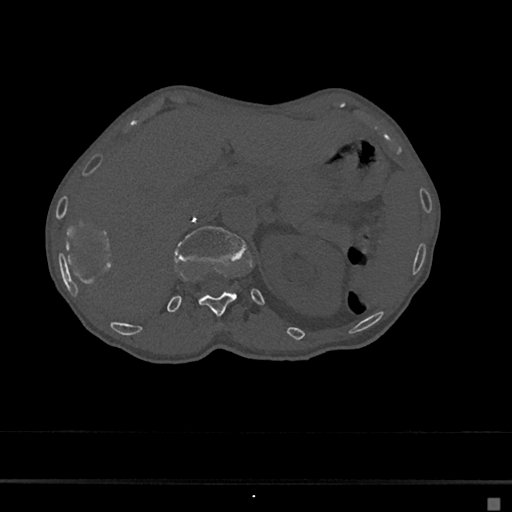
CT including the spine, one axial slice. Slice 111 of 797 in the series (ordered by position). 120 kVp. Bone window (W 1800 / L 400 HU). 0.5 mm slice thickness. 512 × 512 image matrix. Patient: female, 68 years. Case-level facts recorded for this patient, not image findings: primary cancer: renal.
Structures marked on this image (semi-automatically segmented with operator editing):
- L1 vertebra: bounding box (x1, y1, x2, y2) in pixels: (174, 226, 248, 260)
- T12 vertebra: (198, 268, 237, 316)